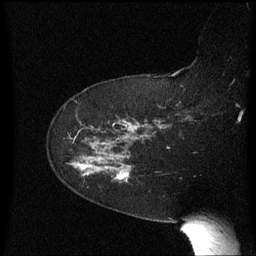
Breast MRI (dynamic contrast-enhanced), one sagittal slice. Slice 43 of 60 in the series (ordered by position). Dynamic contrast-enhanced series, image 2 of 3 at this slice position (ordered by acquisition). 1.5 T. TE 4.2 ms, TR 8.4 ms. 2.3 mm slice thickness. 256 × 256 image matrix. Patient: female, 63 years. Case-level facts recorded for this patient, not image findings: setting: breast cancer imaged before/during neoadjuvant chemotherapy; receptor status: HER2-positive.
Outlined on this slice (semi-automatic segmentation, software-assisted and operator-edited):
- analysis volume of interest (the breast-tissue region the enhancement analysis was run in; not a lesion): box from (x=69, y=136) to (x=138, y=193) px
- tumour enhancement mask (voxels above the 70 % enhancement threshold inside the analysis volume of interest): (x=81, y=166)–(x=125, y=181)